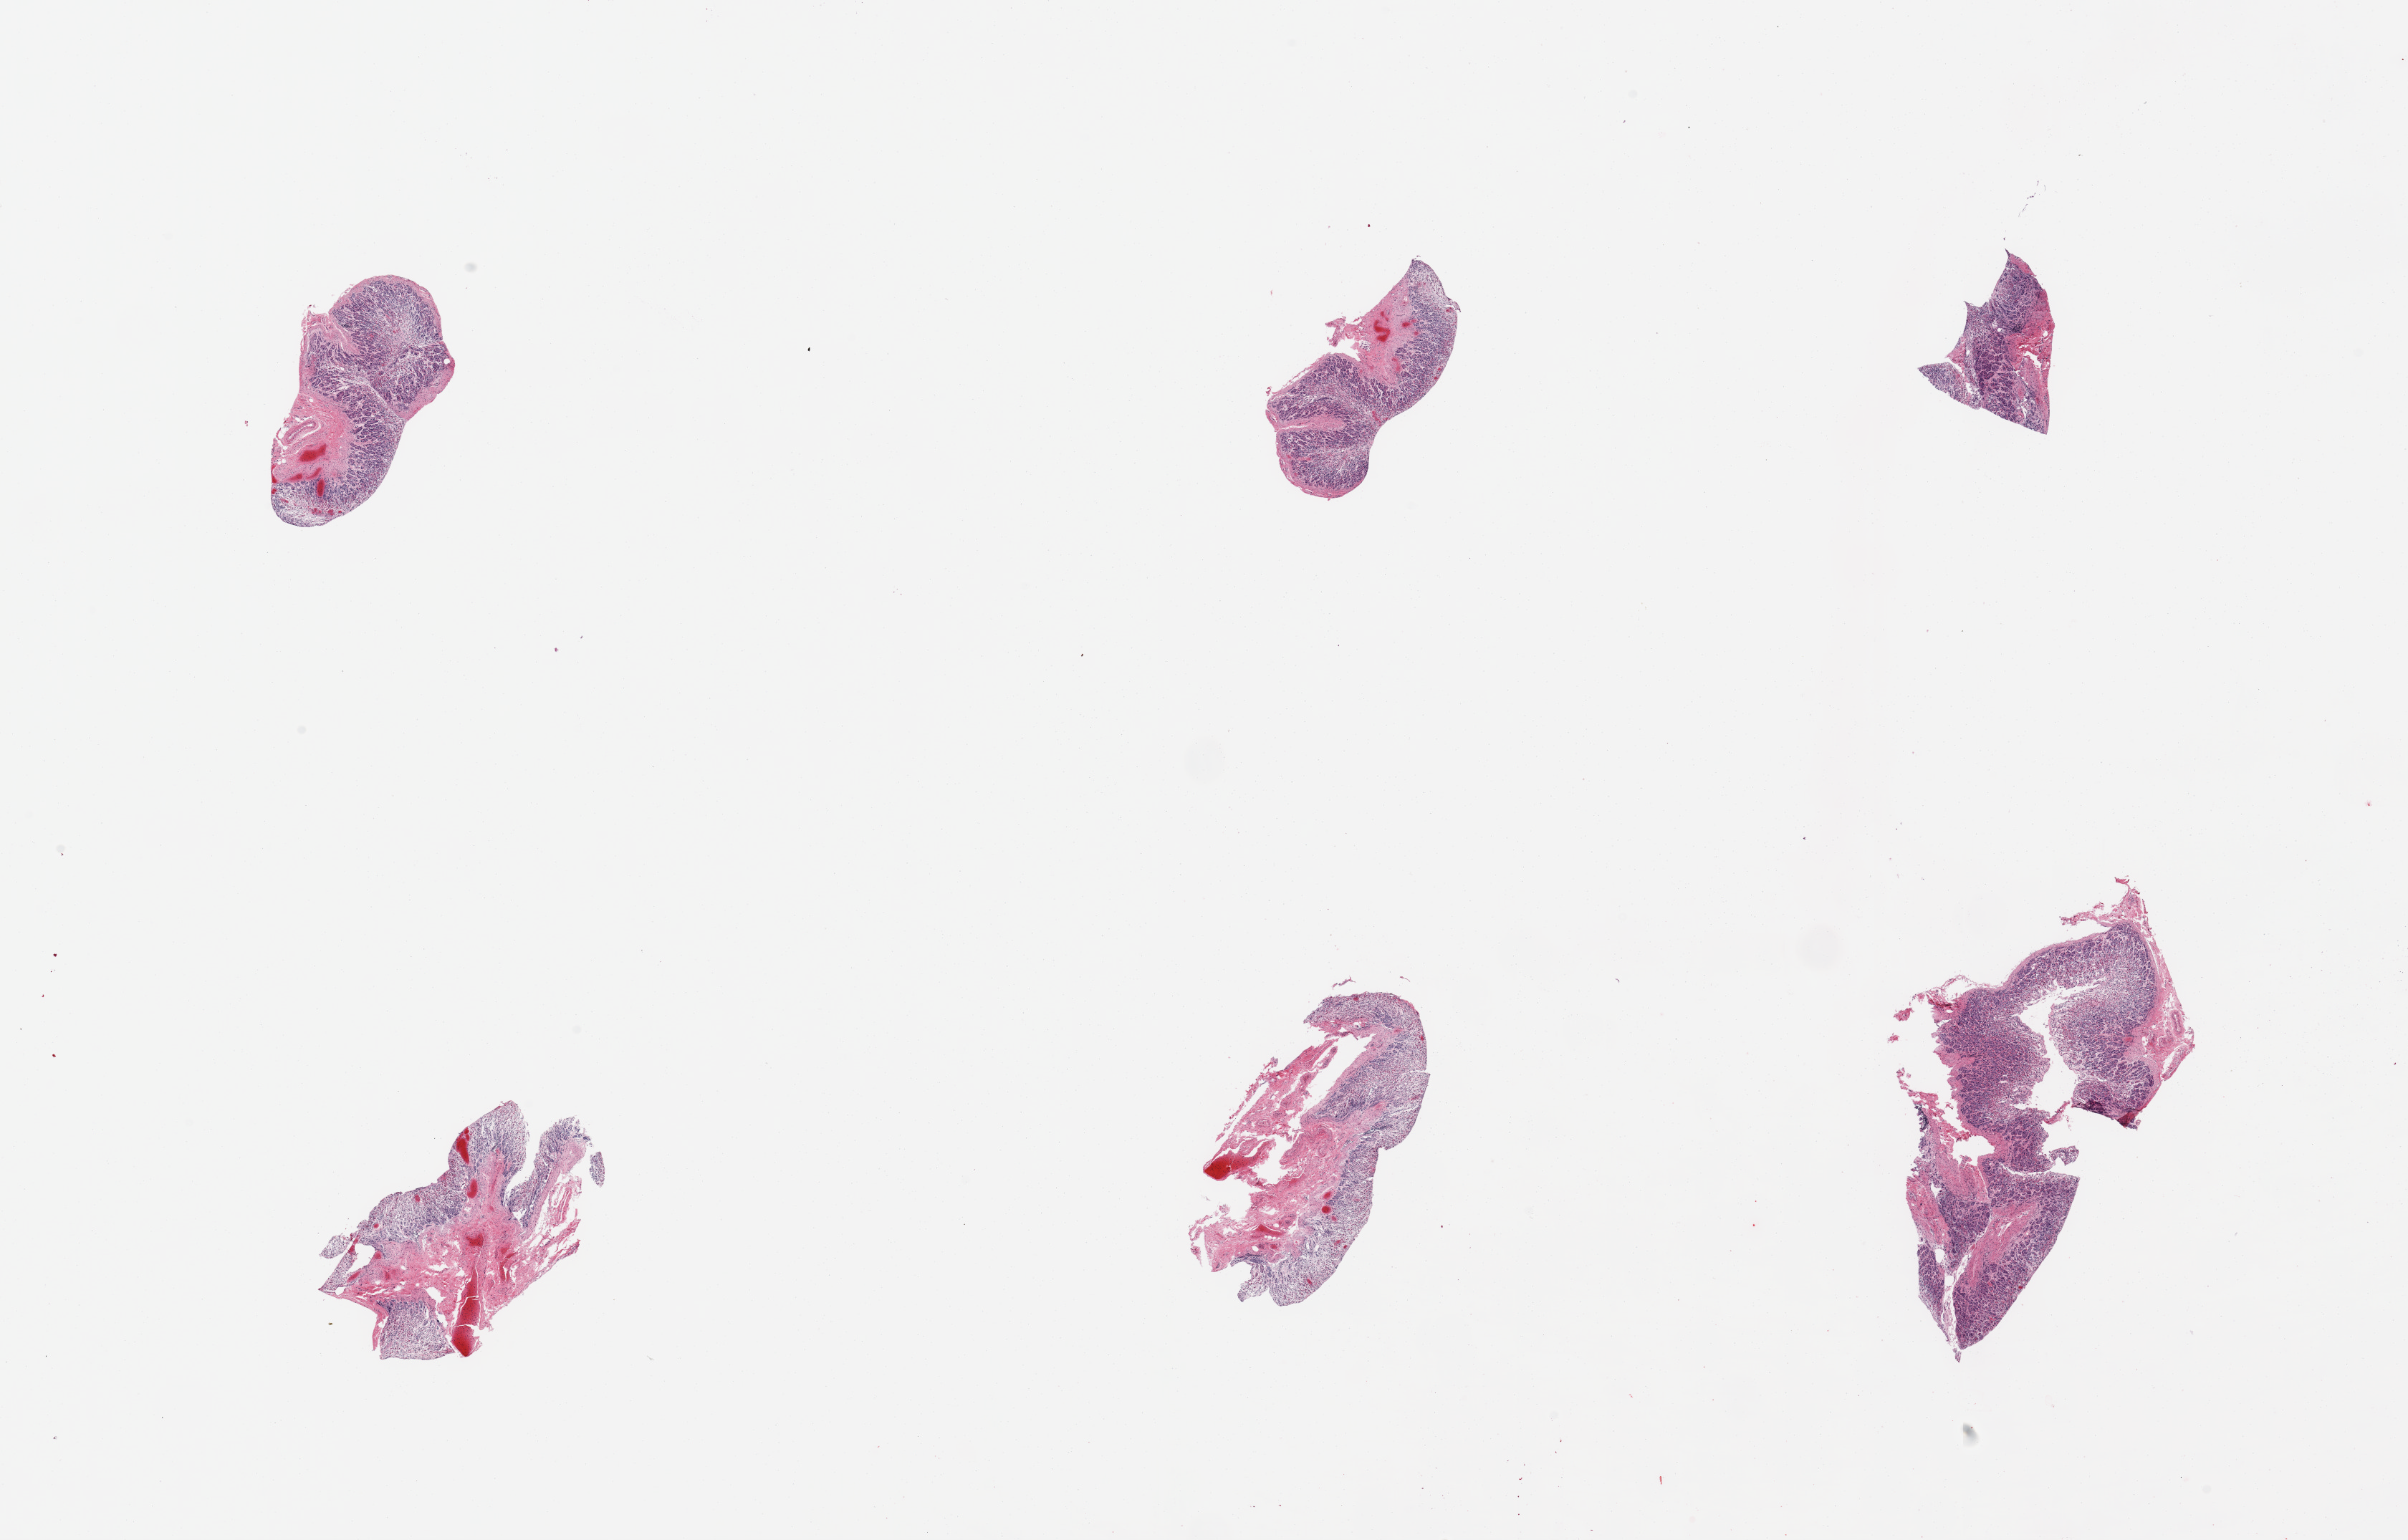
Whole-slide image, haematoxylin and eosin stain — whole scanned area (about 26.6 x 17.0 mm, slide scanned at 20x) shown as a low-resolution overview, PAXgene-fixed, paraffin-embedded tissue, target tissue: gastroesophageal junction, donor tissue sample.
Reviewer comment on this tissue sample: 6 pieces, autolyzing gastric mucosa; no muscularis present.